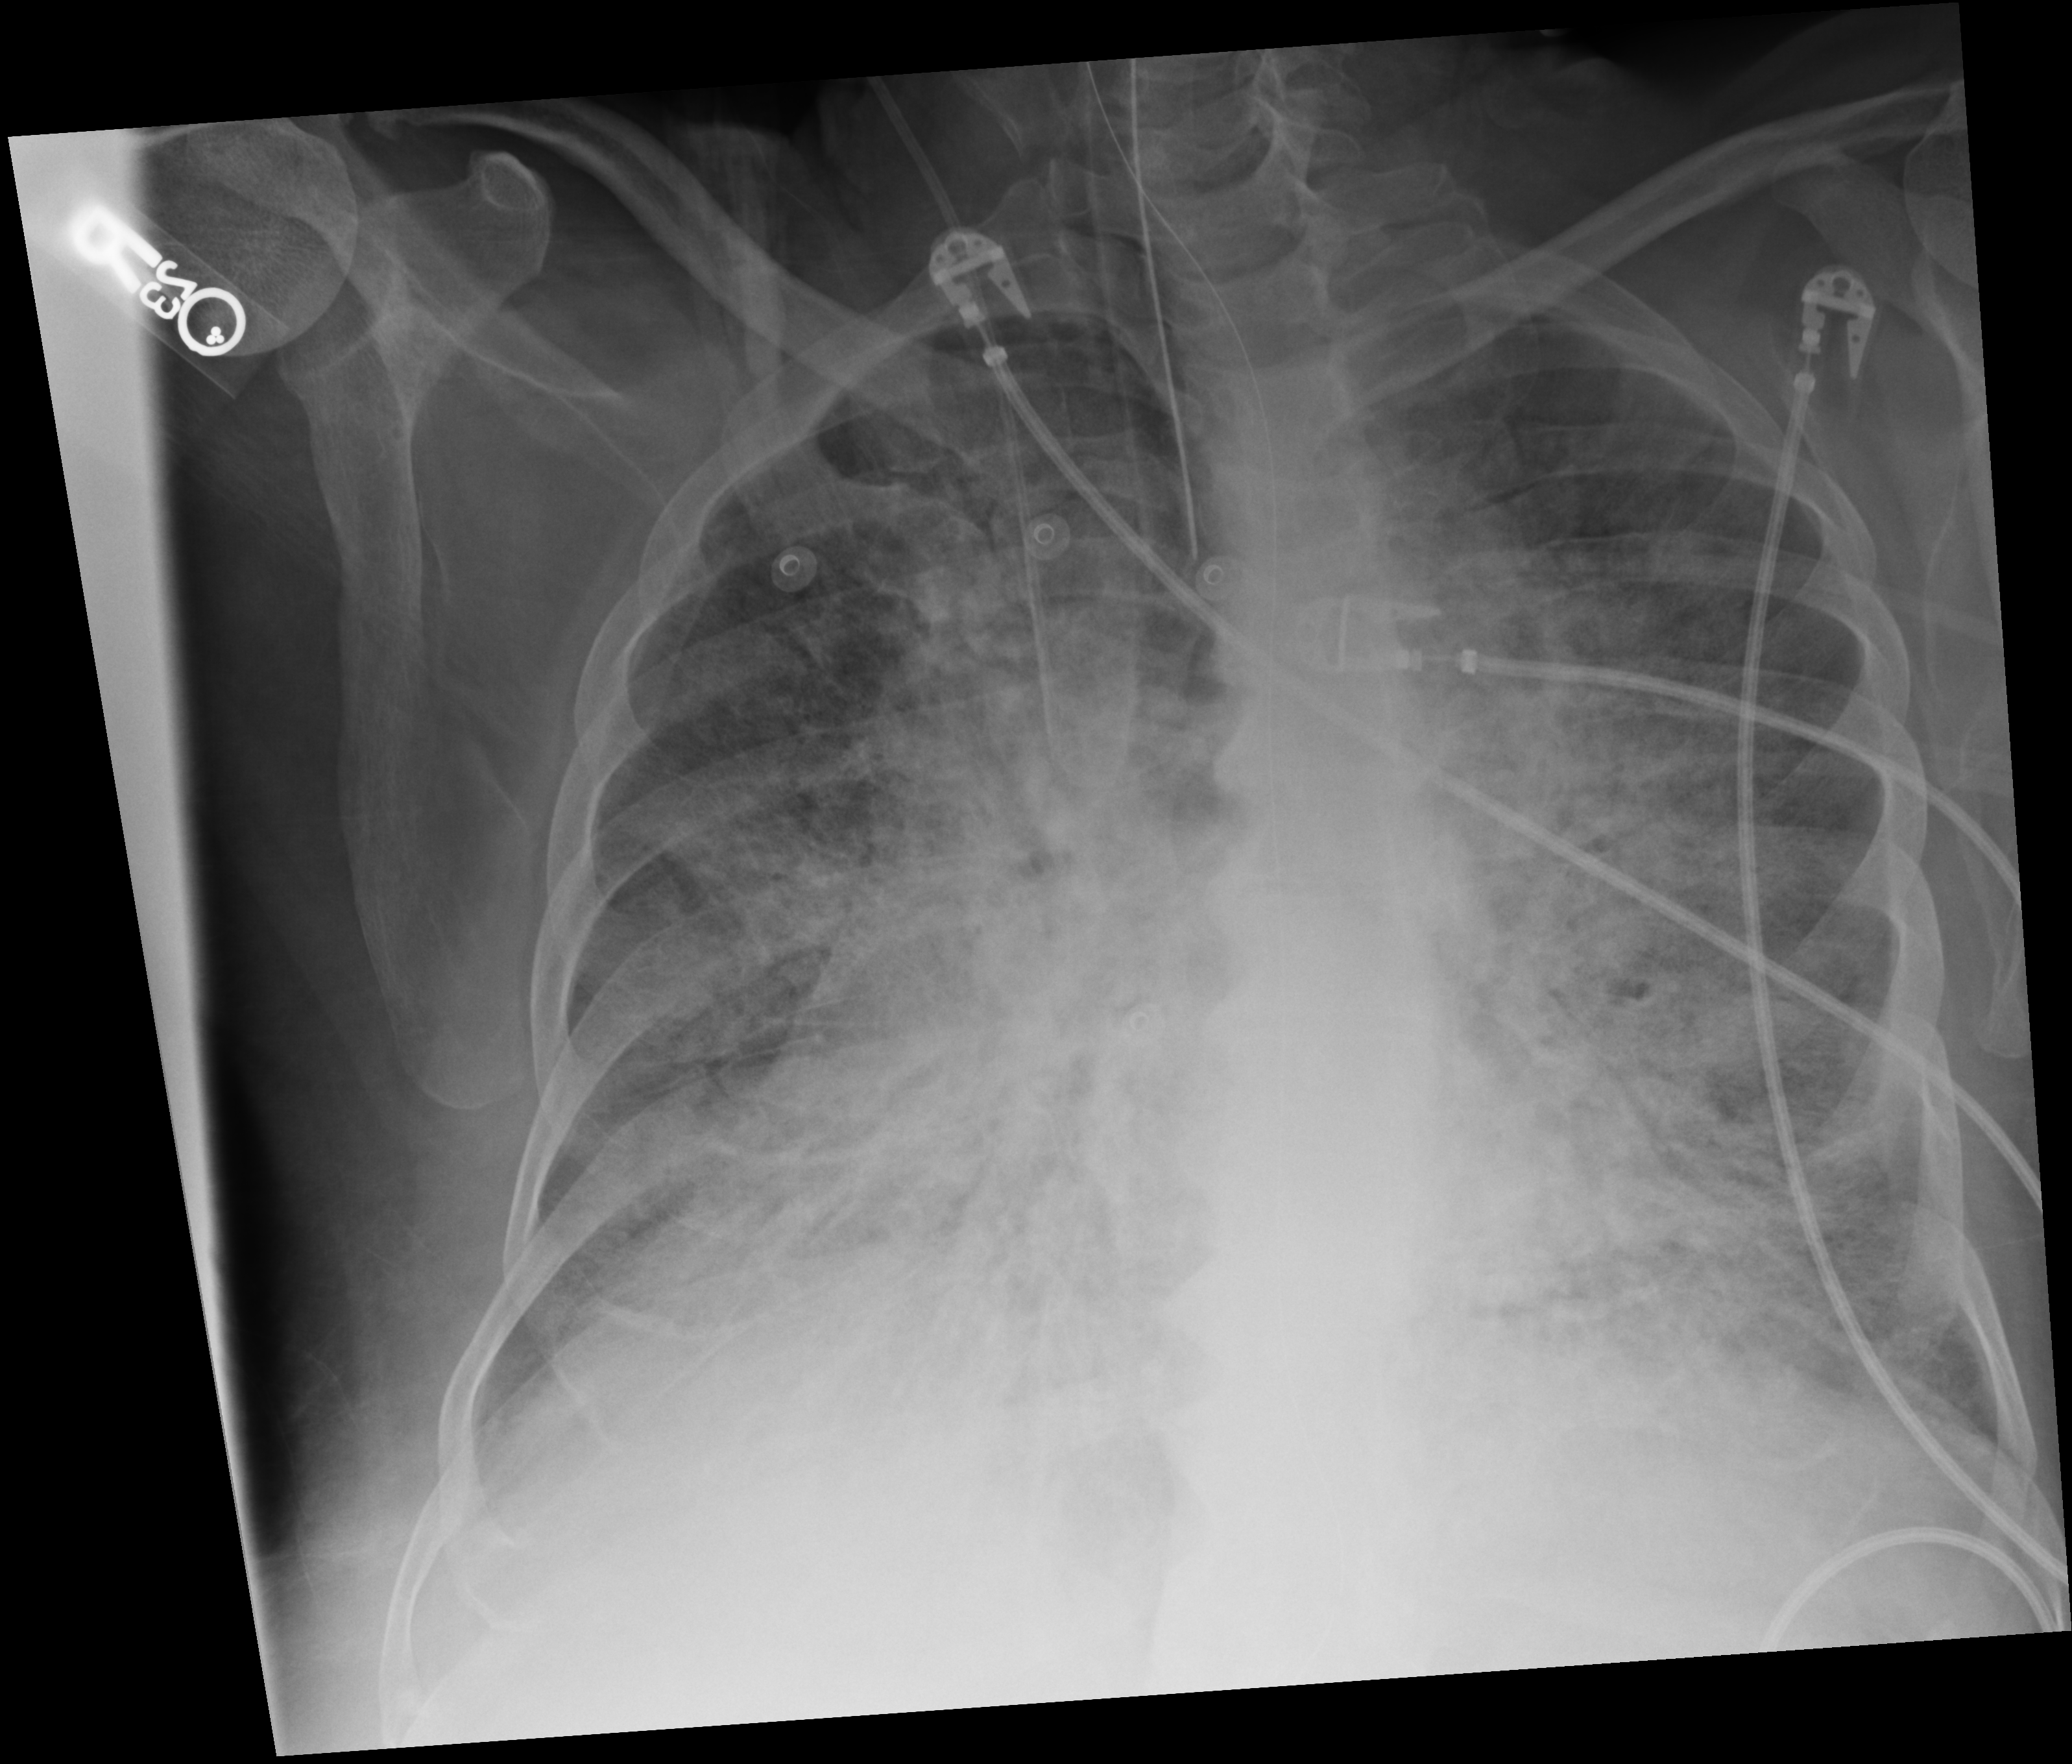
Portable chest radiograph. Male patient hospitalised with COVID-19, age 60–74 years.
From the hospital-stay record, not from the radiograph (when in the stay this image was taken is not recorded): smoking status (admission record): never.